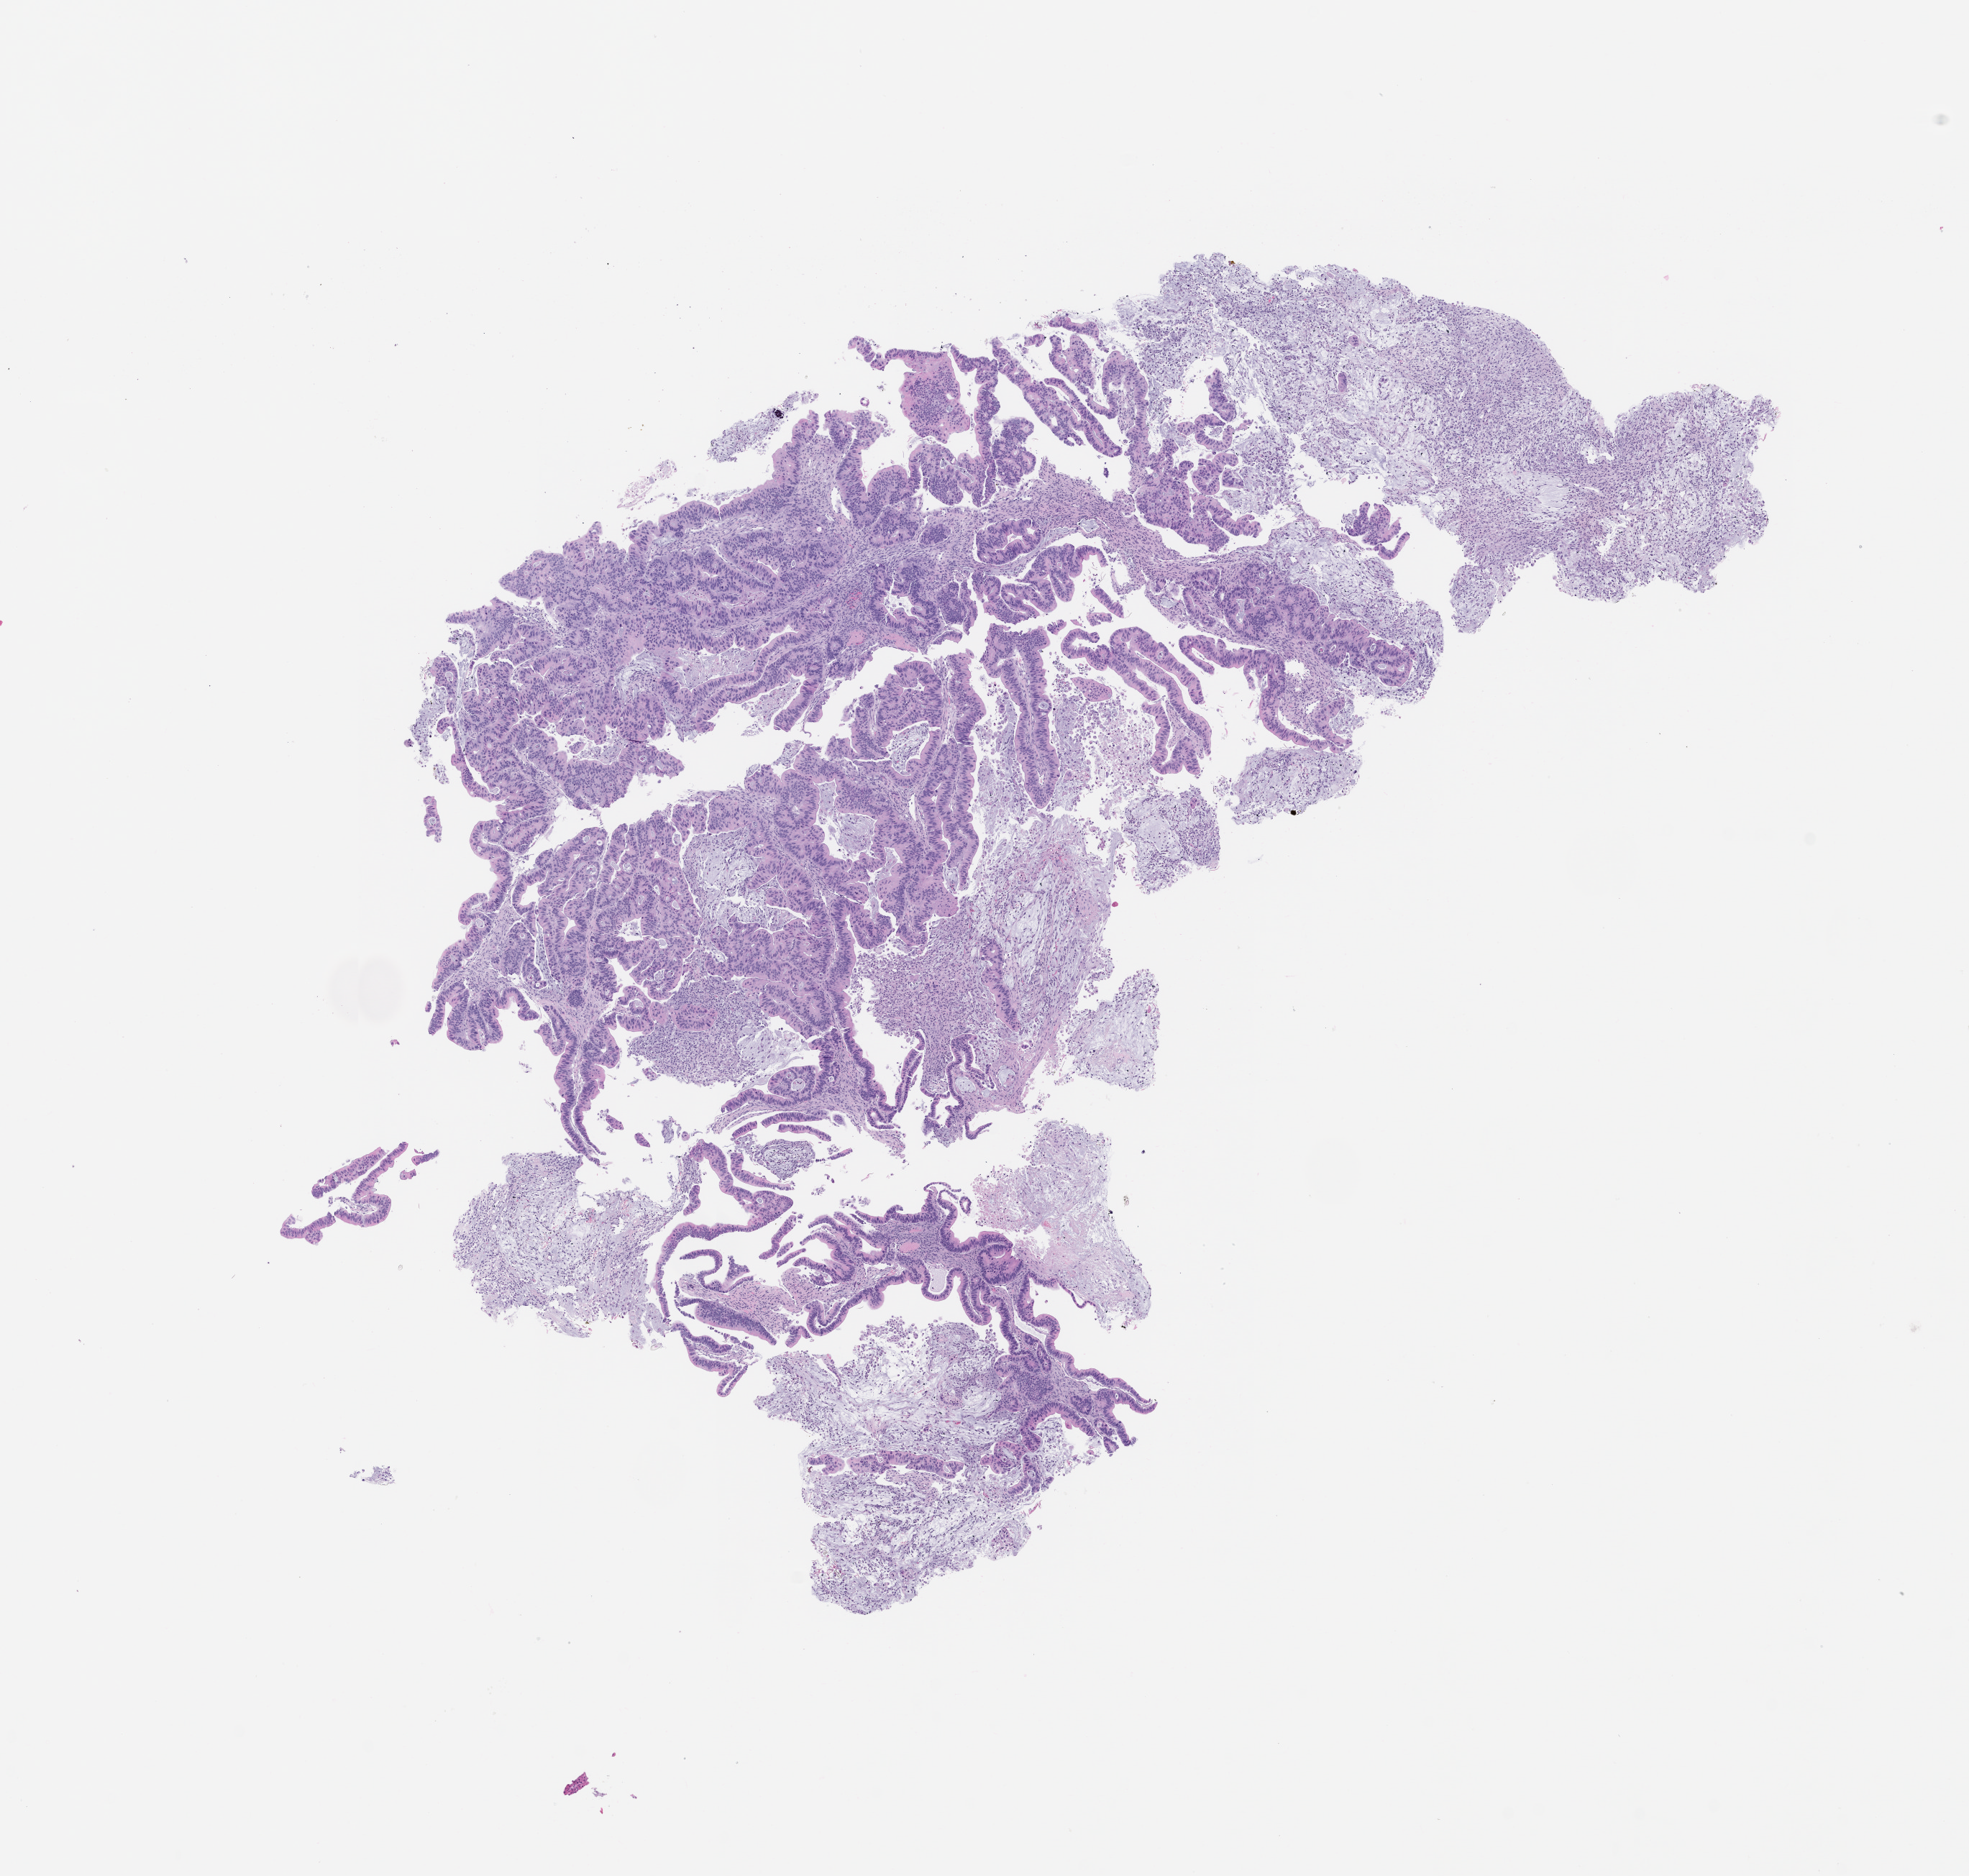
Haematoxylin and eosin whole-slide image of a patient-derived xenograft (PDX) tumor grown in a mouse, passage 2, shown as a low-resolution overview of the whole scanned area (about 11.0 x 10.5 mm); formalin-fixed, paraffin-embedded (FFPE) tissue; originating tumor site category: colon.
Originating patient diagnosis: Colon Adenocarcinoma.